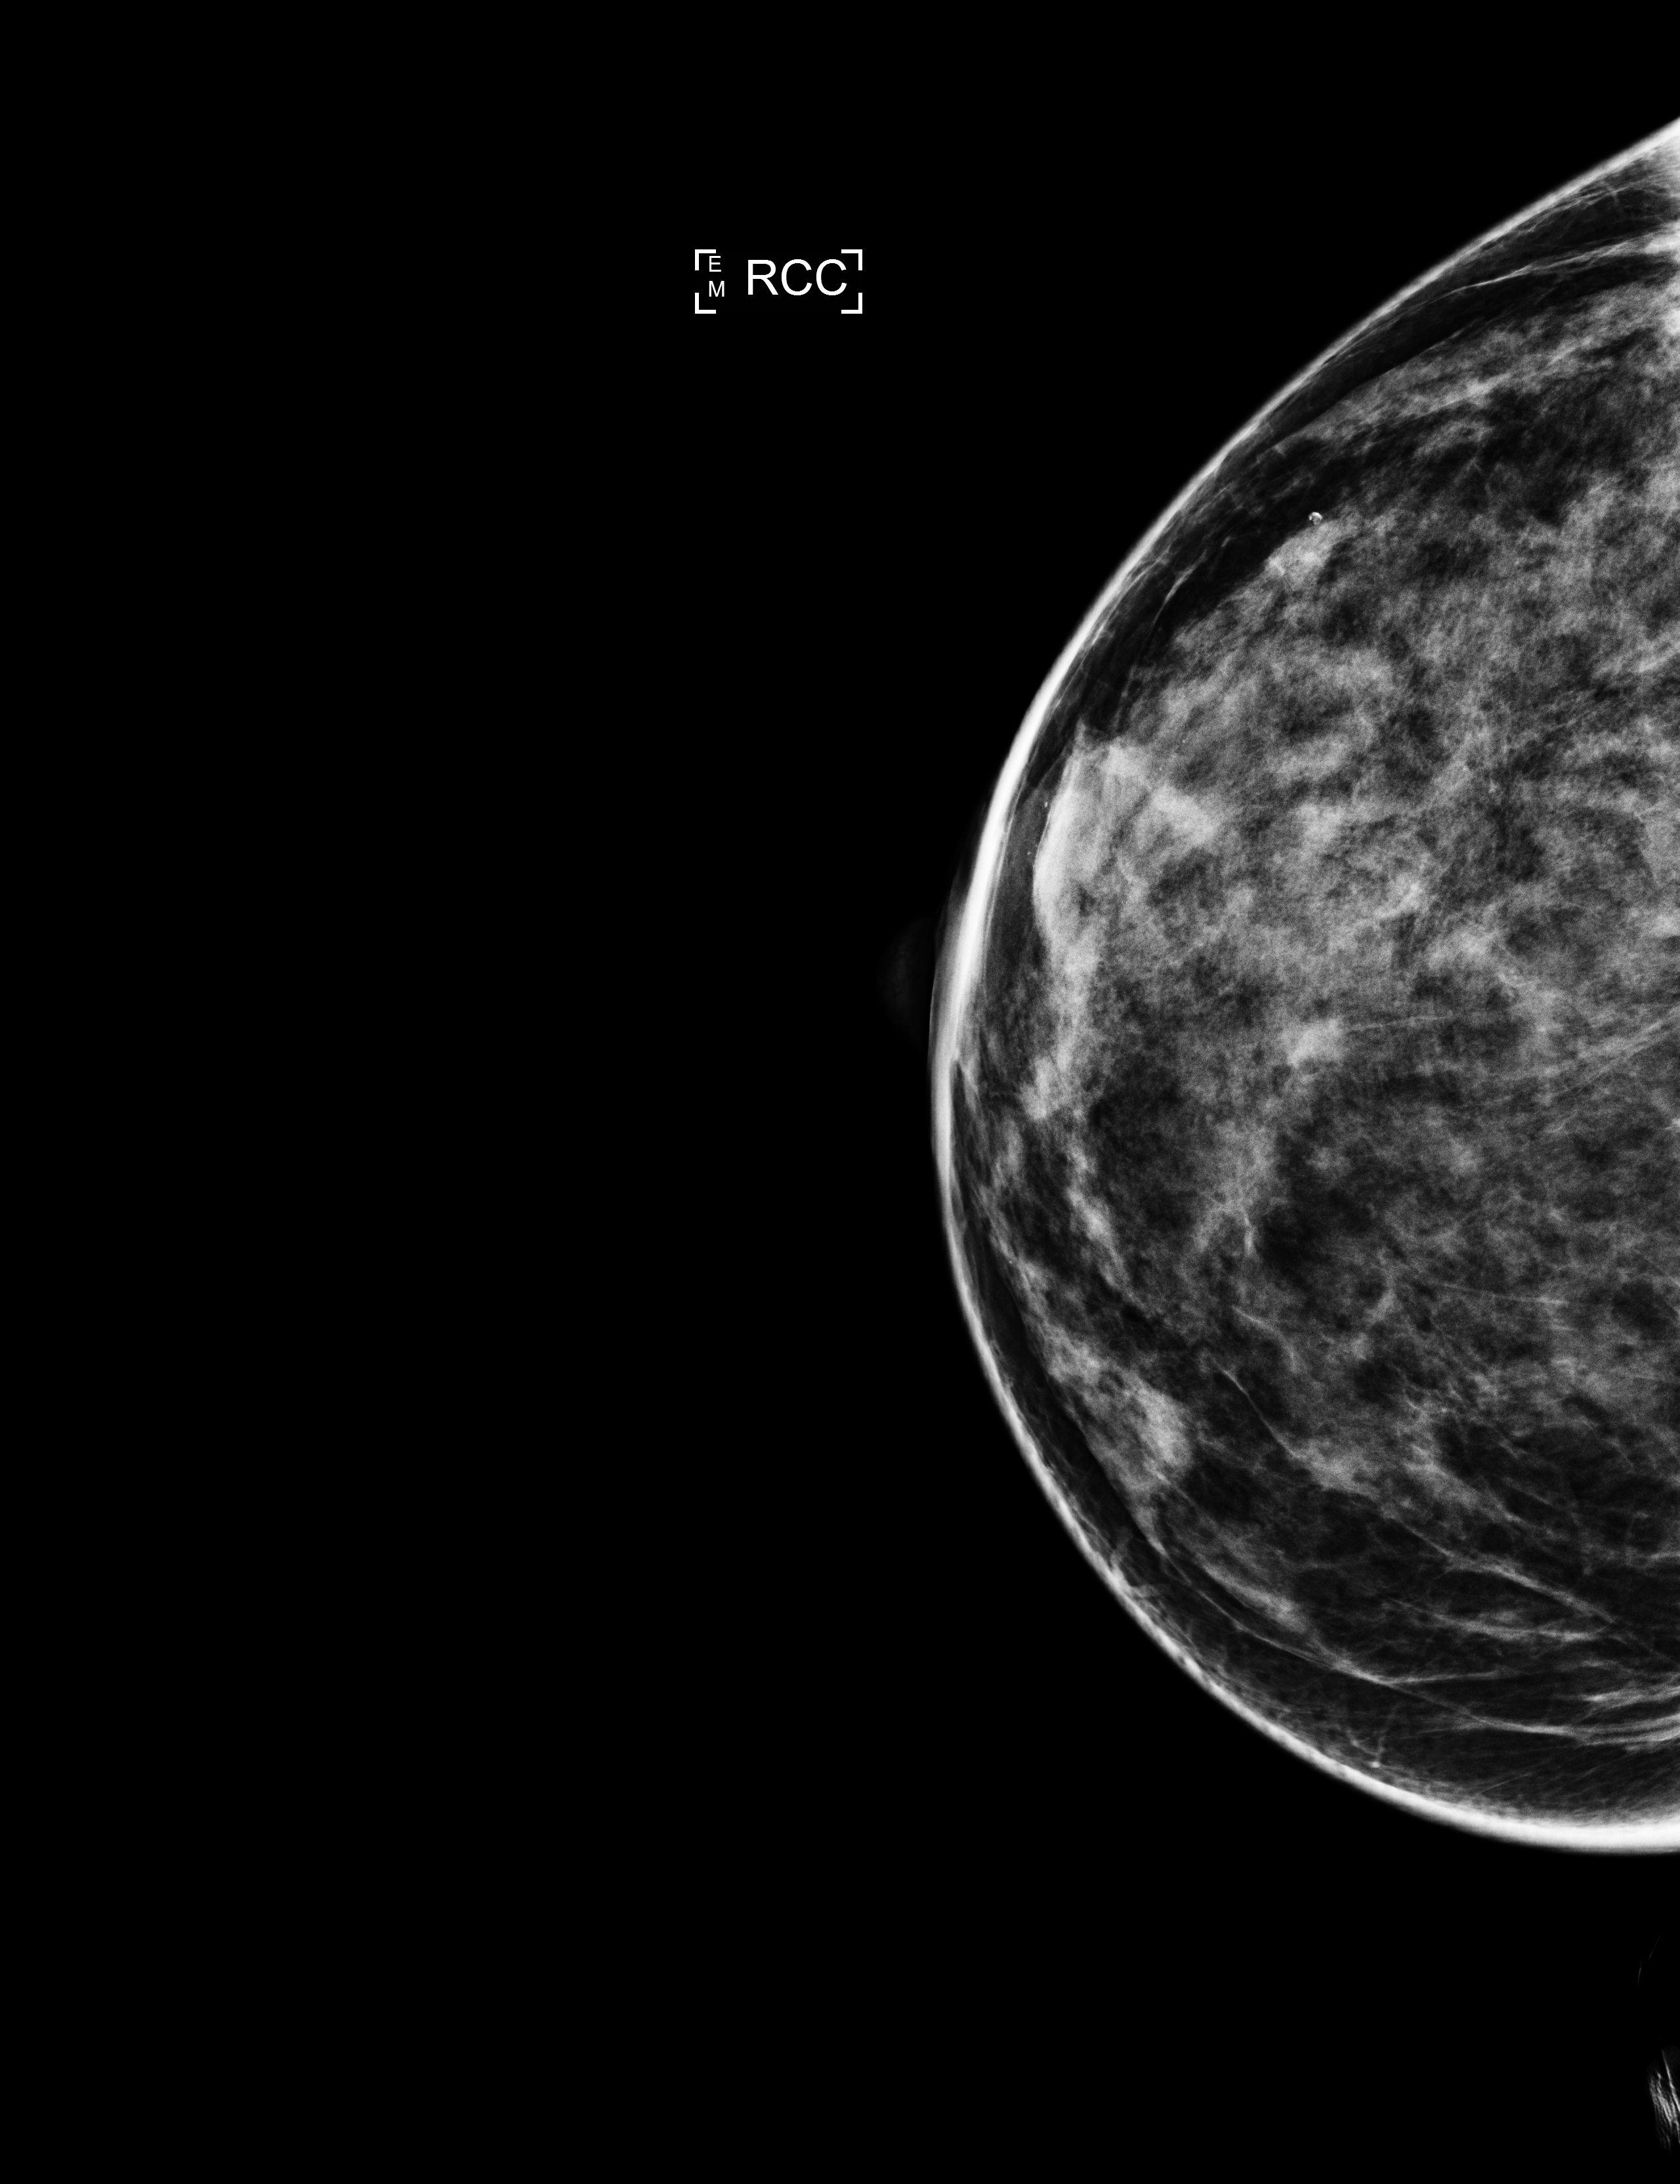
Screening examination, compressed breast thickness 52 mm, system: Selenia Dimensions. Patient aged 44 years (female).
Image type: full-field digital mammogram. Breast: right. Projection: cranio-caudal projection.